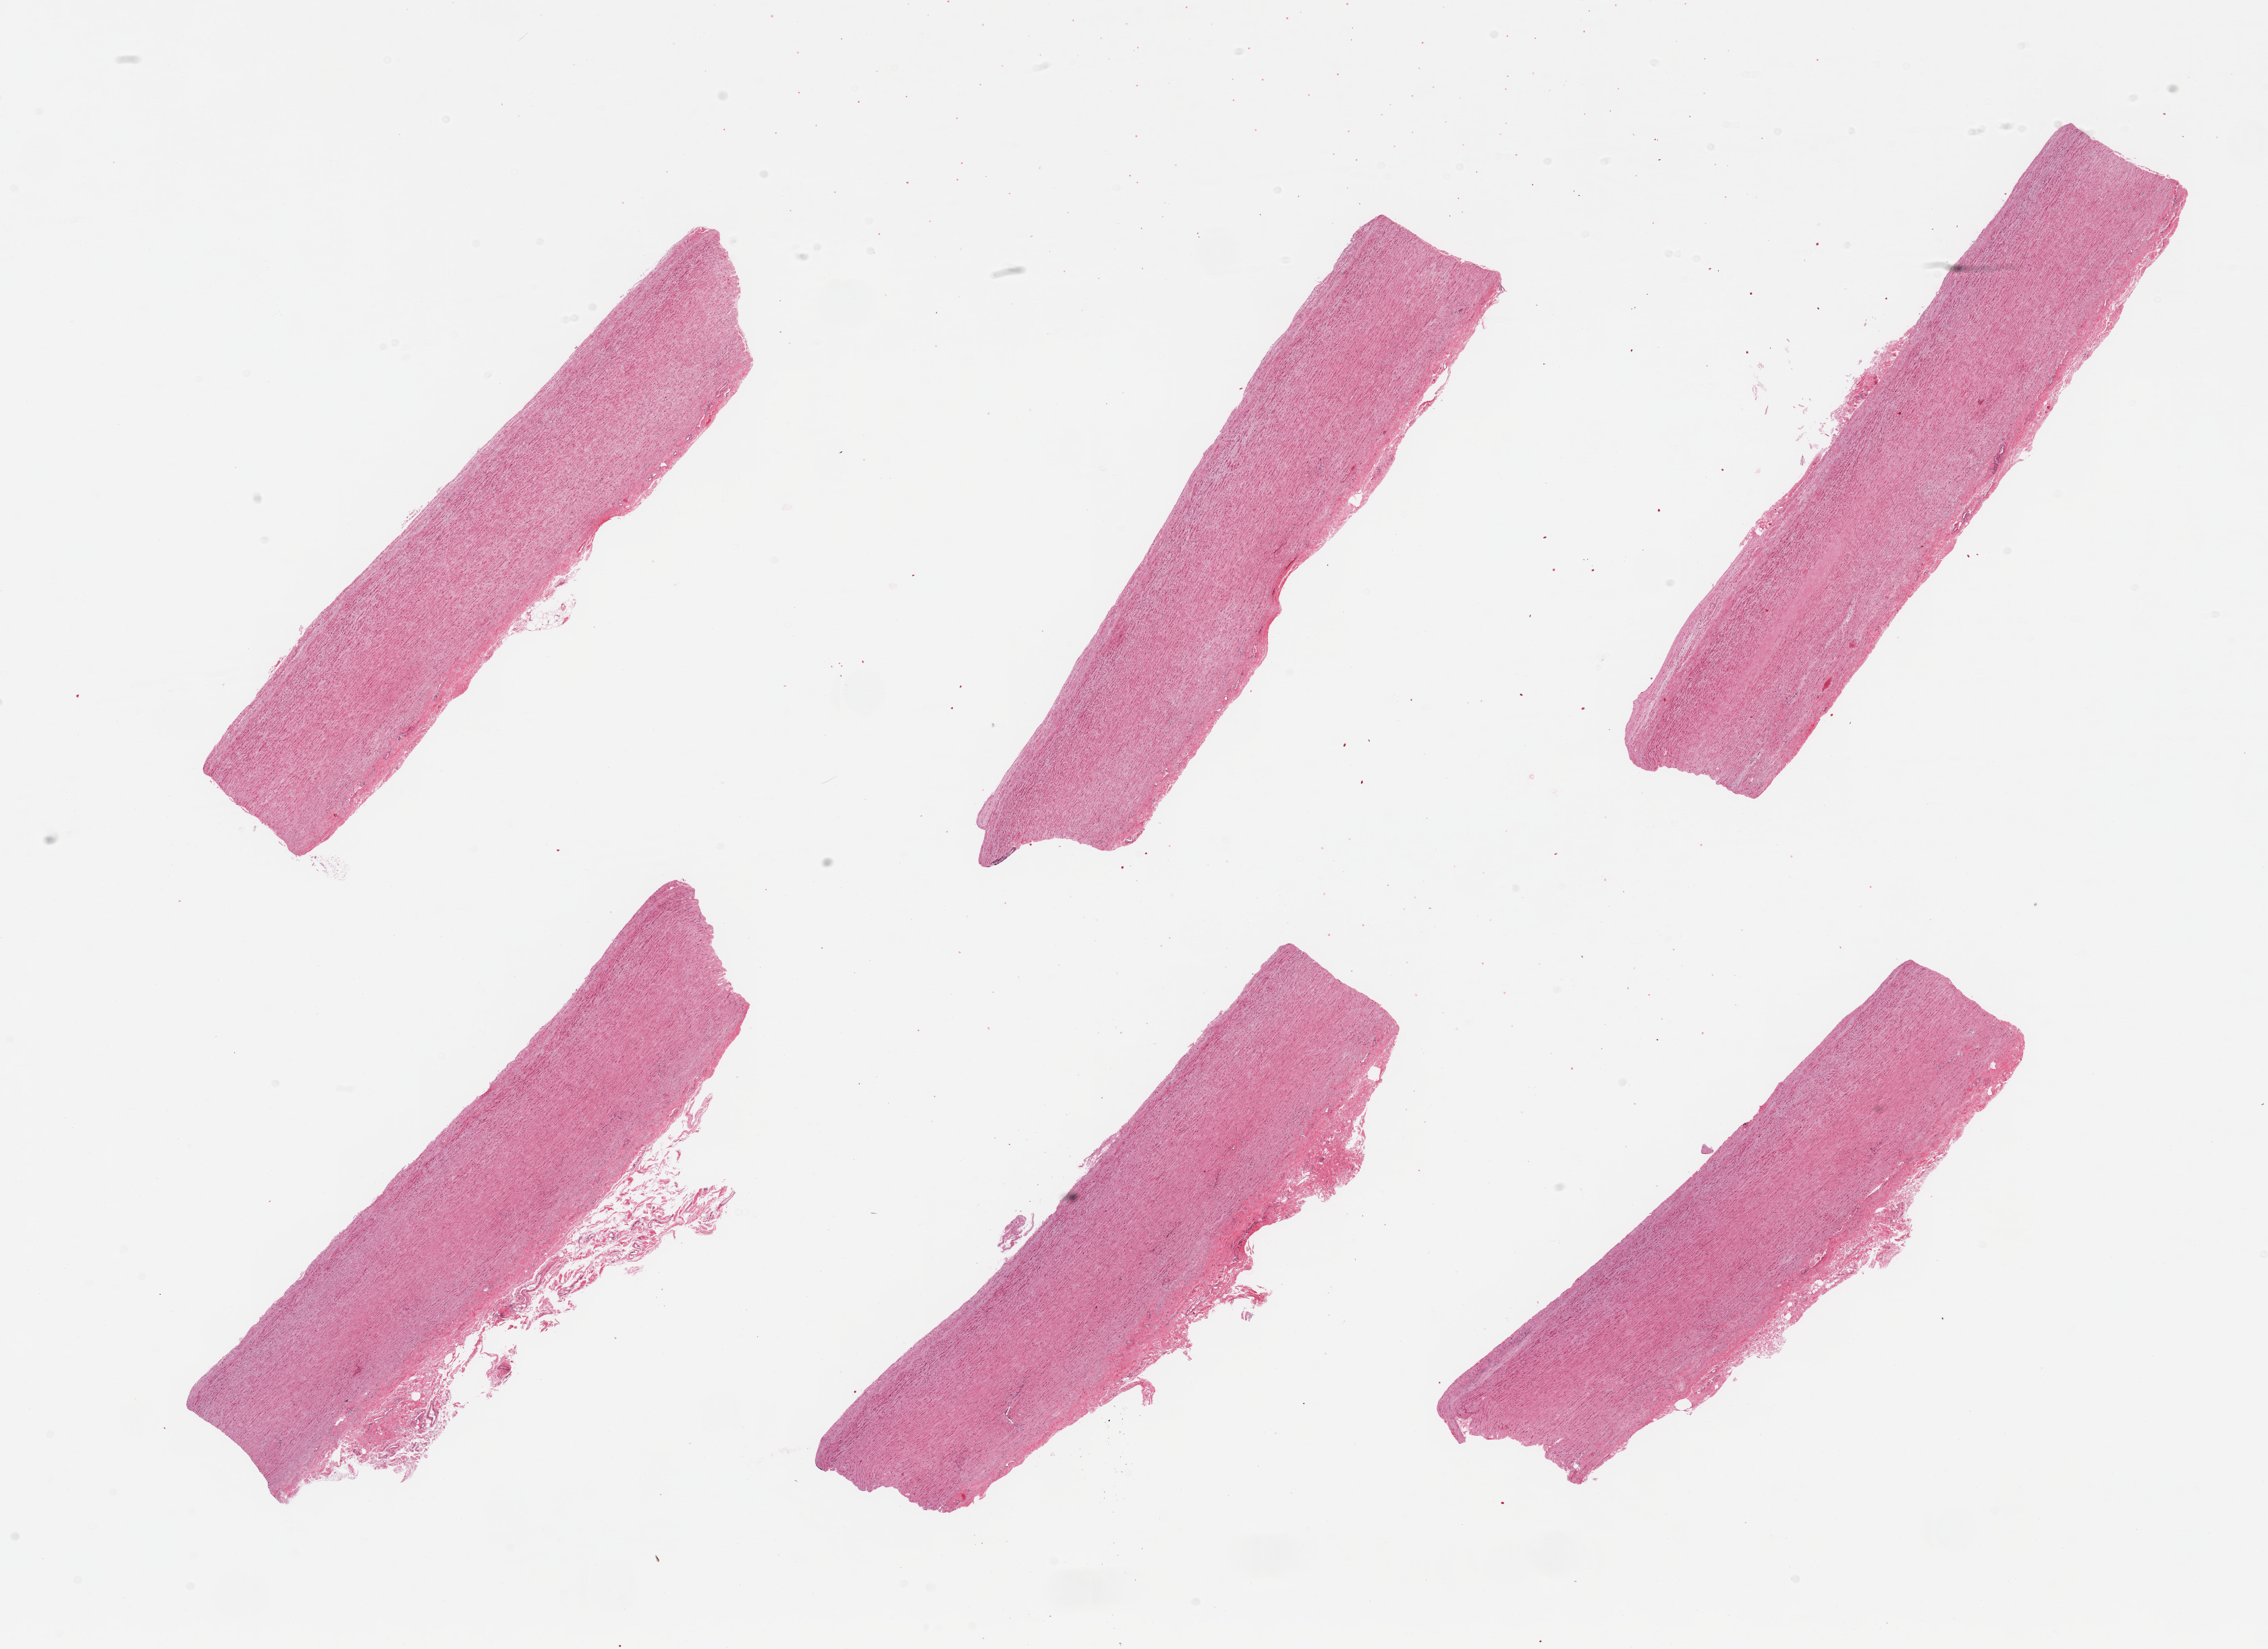
Whole-slide image, haematoxylin and eosin stain, shown as a low-resolution overview of the whole scanned area (about 26.6 x 19.3 mm), PAXgene-fixed paraffin-embedded (PFPE) section, target tissue: aorta, tissue donor sample. Male donor.
* reviewer comment on this tissue sample: 6 pieces; minimal plaque; well trimmed adventitia